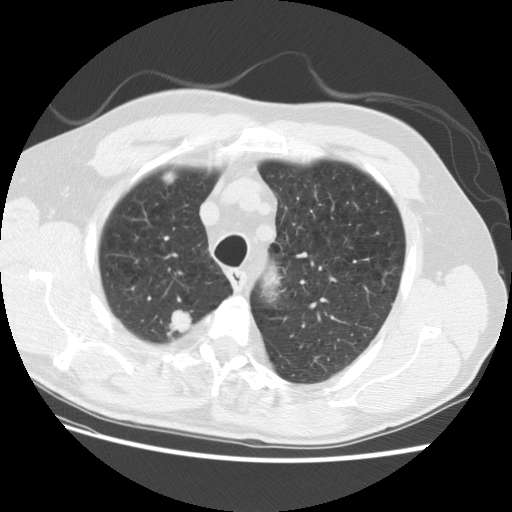
Chest CT (low-dose screening protocol), one axial image, baseline annual screen, lung window (W 1500 / L -600 HU), standard (soft-tissue) reconstruction kernel (STANDARD), 140 kVp, slice 25 of 124 in the series, 512 × 512 image matrix. Male, age 69 years at enrolment.
• Expert reader's lesion annotation, bounding box <158,305,201,341> (left, top, right, bottom; pixels).
• Screening reader's record for this exam (one nodule recorded; not confirmed to be the boxed lesion): non-calcified nodule or mass ≥4 mm, right upper lobe, 15 × 15 mm, spiculated (stellate) margins, soft tissue attenuation.
• Official screen result: positive, change unspecified: nodule(s) >= 4 mm or enlarging nodule(s), mass(es), or other non-specific abnormalities suspicious for lung cancer.
• Later outcome: lung cancer diagnosed 22 days after this screen — large cell neuroendocrine carcinoma, right upper lobe, poorly differentiated (G3), stage IA (AJCC 6th edition), 23 mm at pathology.